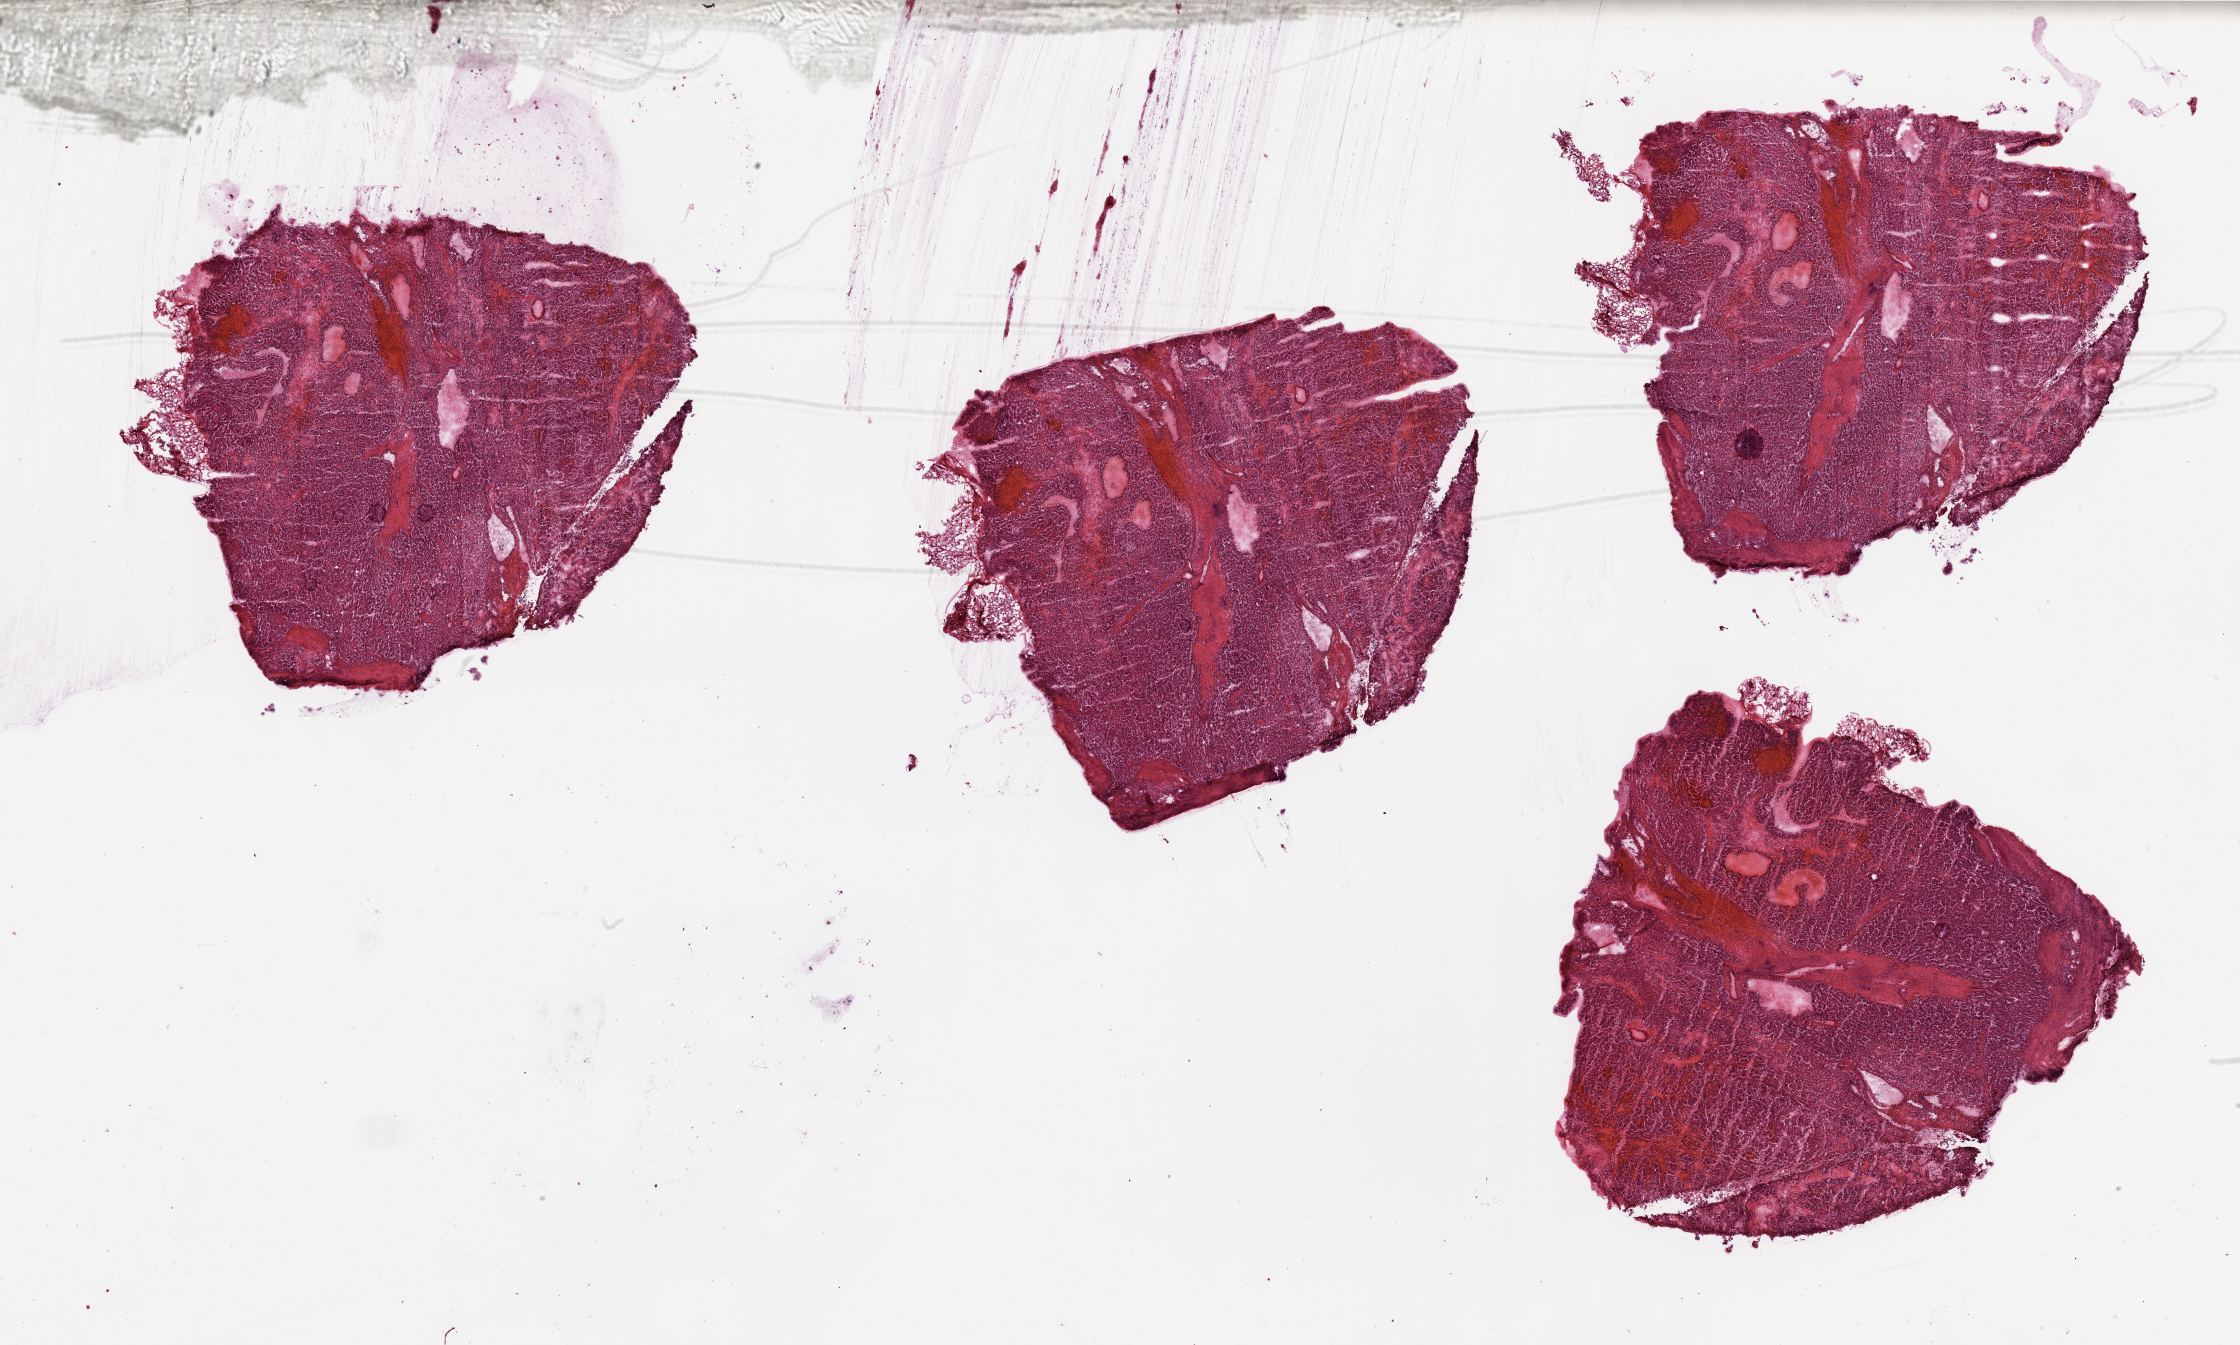
Whole-slide histology image, H&E-stained — shown as a low-resolution overview of the whole scanned area (about 35.4 x 21.3 mm, acquisition: 20x scan), tumour tissue sample, sampled site: kidney. 60-year-old female patient. Histologic grade: G1 (well differentiated). Slide review estimates, as recorded: tumour nuclei 90%, necrosis 5%.
- diagnosis: Renal cell carcinoma, NOS
- AJCC pathologic stage: I
- primary tumour site (as recorded): middle